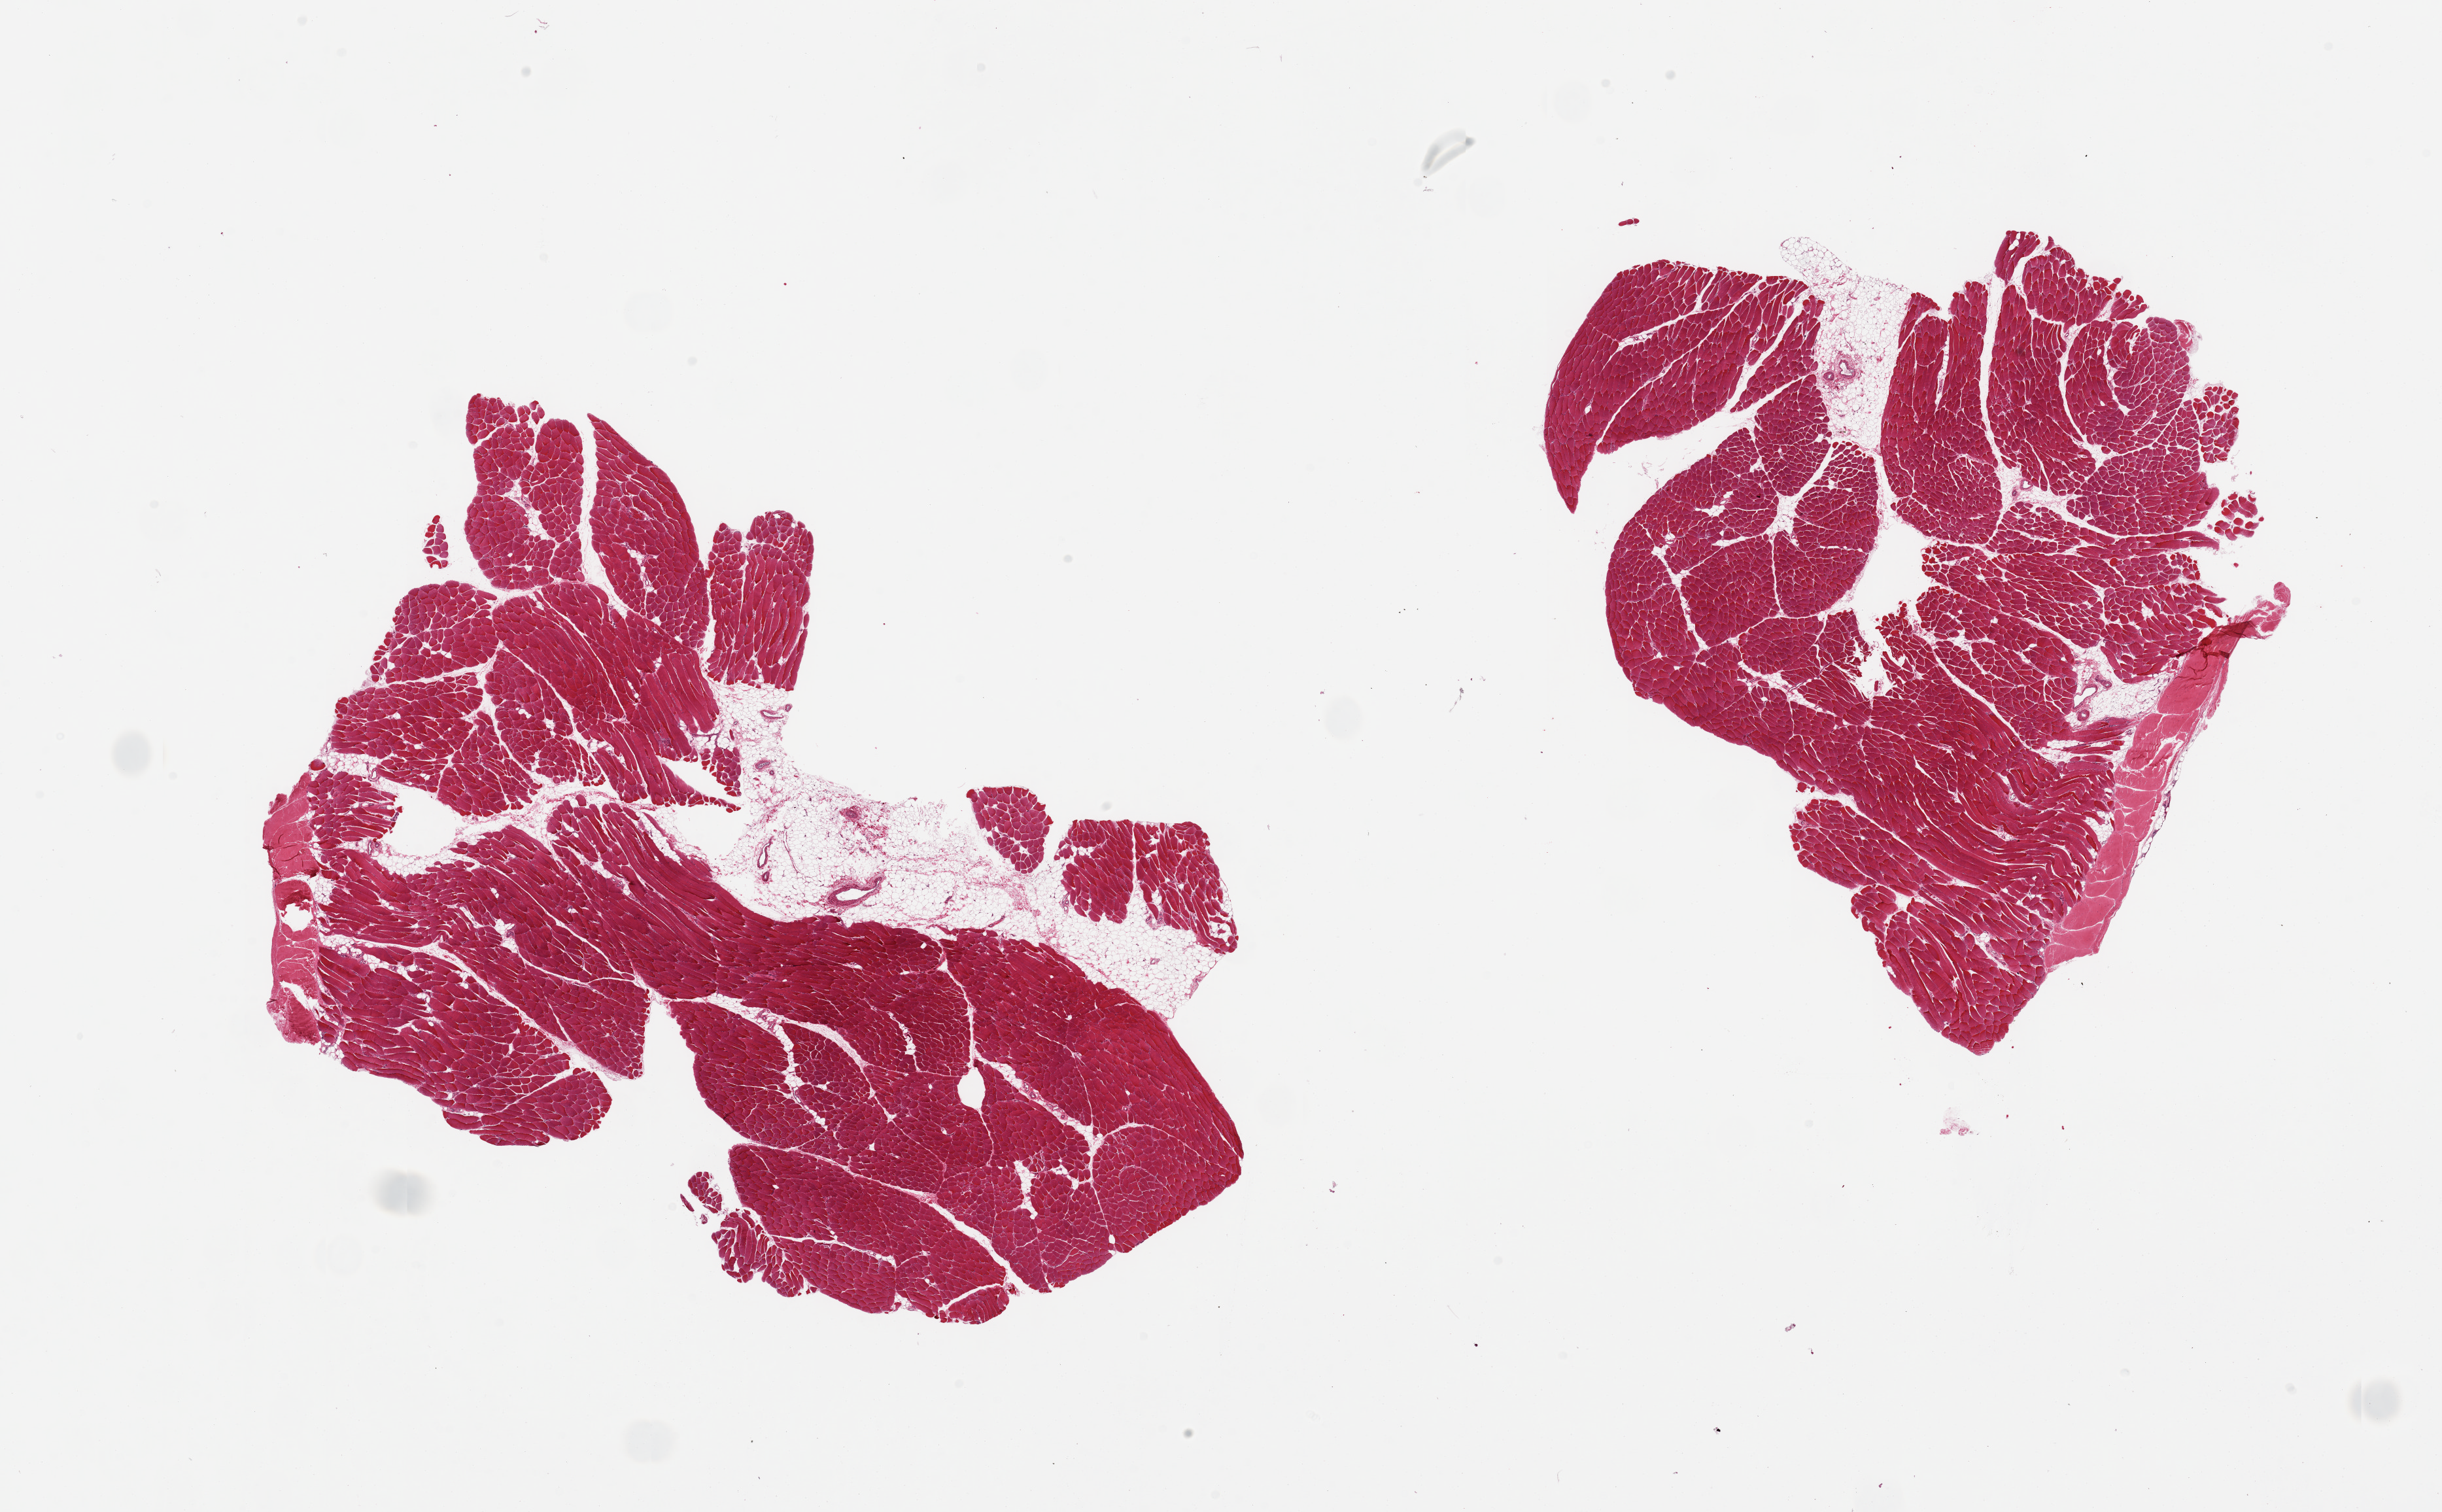
Digitized haematoxylin and eosin-stained section, a low-resolution overview of the entire scanned area, about 29.5 x 18.3 mm. PAXgene-fixed, paraffin-embedded tissue. Target tissue: skeletal muscle. Tissue donor sample.
* pathologist's review note for this sample: 2 pieces, ~10-15% interstitial fat or adherent tendon